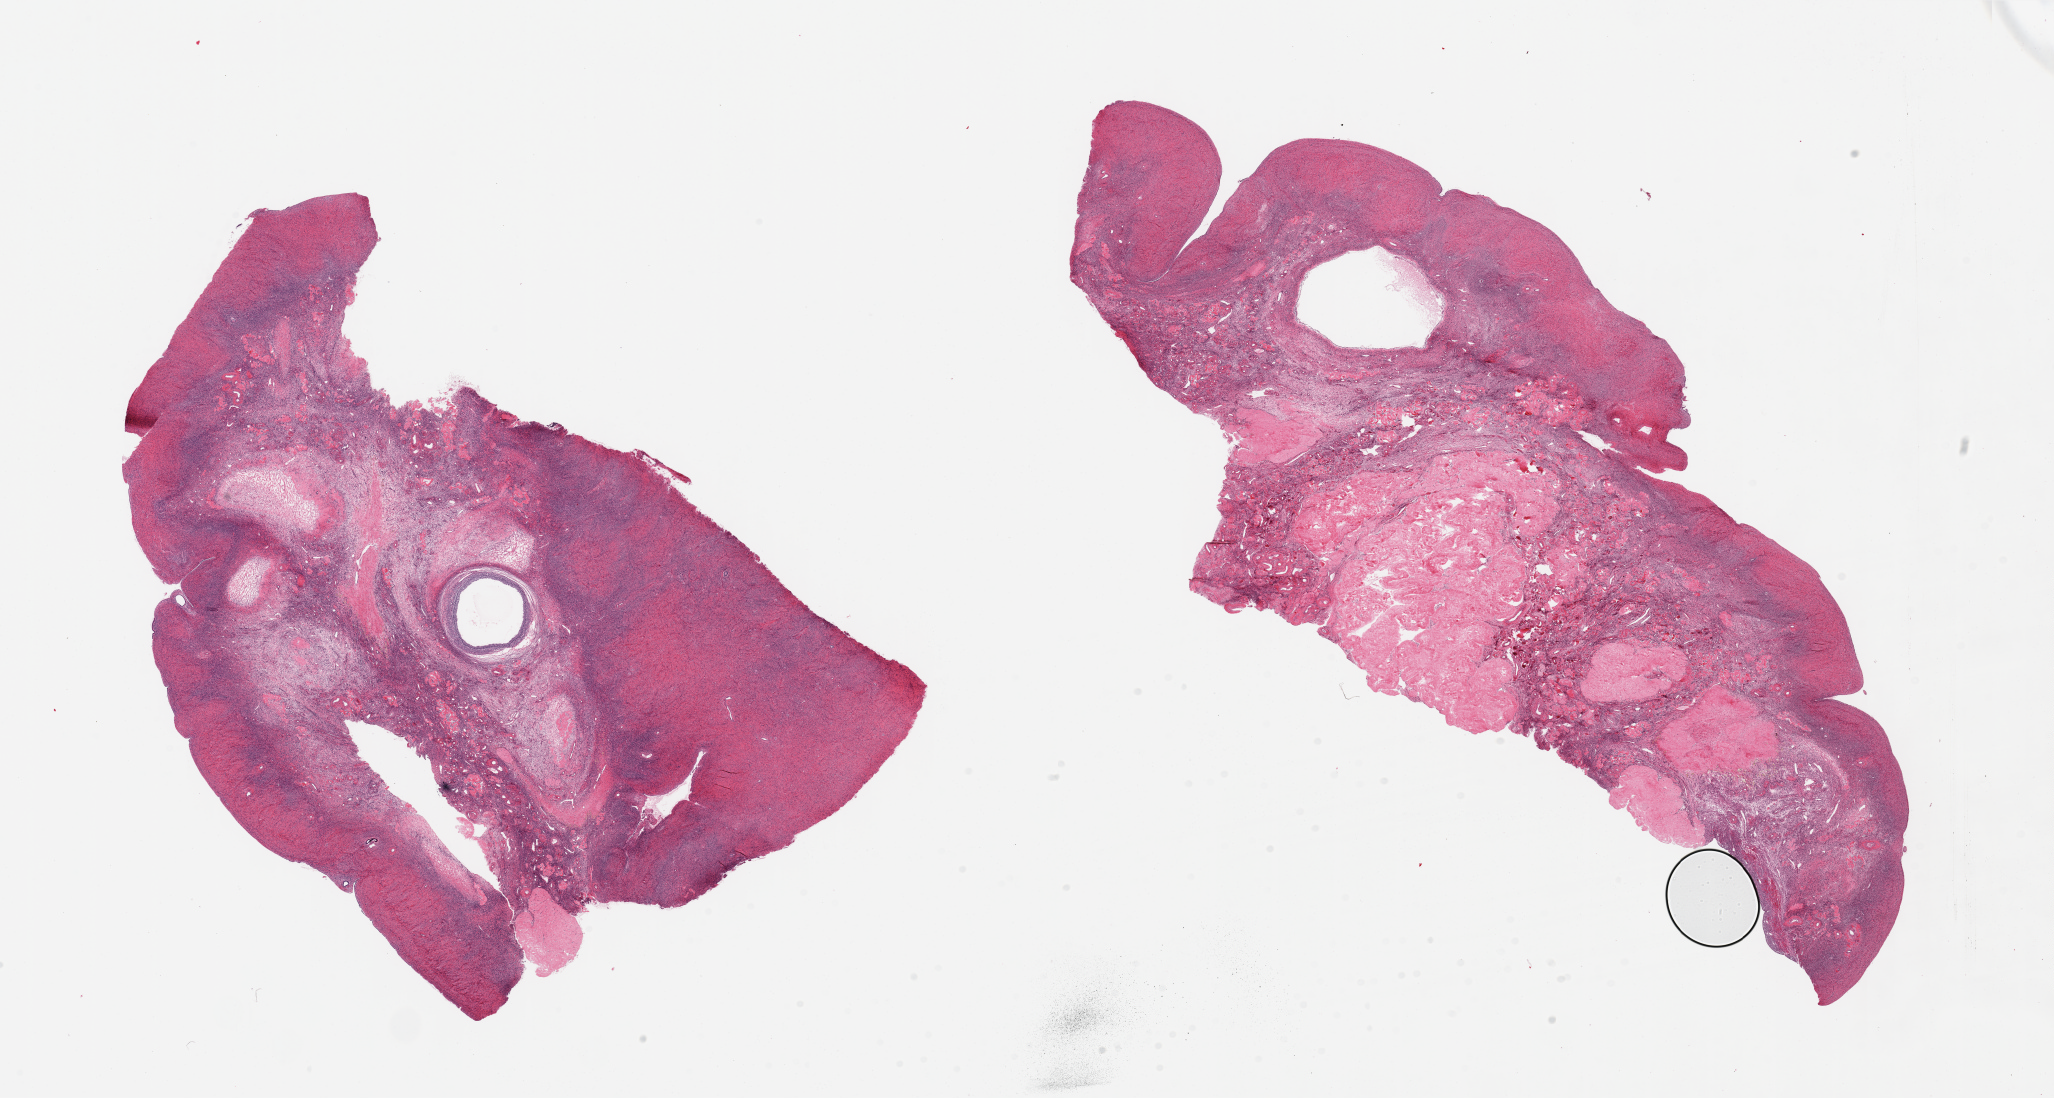
Digitized haematoxylin and eosin-stained section, a low-resolution overview of the entire scanned area, about 32.5 x 17.4 mm; PAXgene-fixed paraffin-embedded (PFPE) section; sampled site (target tissue): ovary; tissue donor sample. Donor: female.
- pathologist's review note for this sample: 2 pieces, 1.5mm follicular cyst, few embedded eggs in cortex